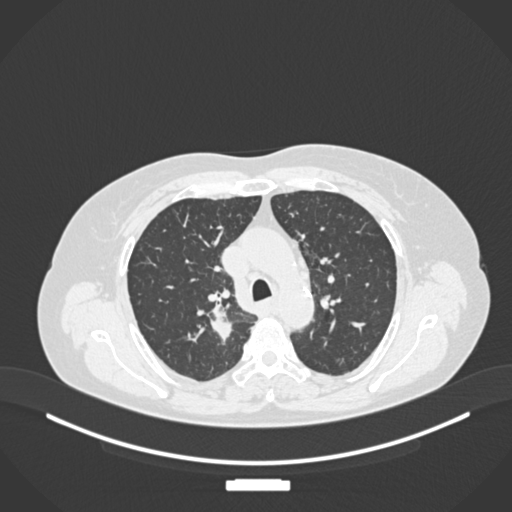
Chest CT, one axial slice. Slice 180 of 237 in the series (ordered by position). Reconstruction kernel B30f. Lung window (W 1500 / L -600 HU). 512 × 512 image matrix, field of view 400 × 400 mm. Female patient, age 62 years. Case-level facts recorded for this patient, not image findings: clinical TNM (as recorded): T1c N1 M0.
Annotated regions visible in this slice (bounding box drawn by a radiologist):
- lung tumour (recorded histology: squamous cell carcinoma): bounding box [x1, y1, x2, y2] px = [208, 298, 237, 344]